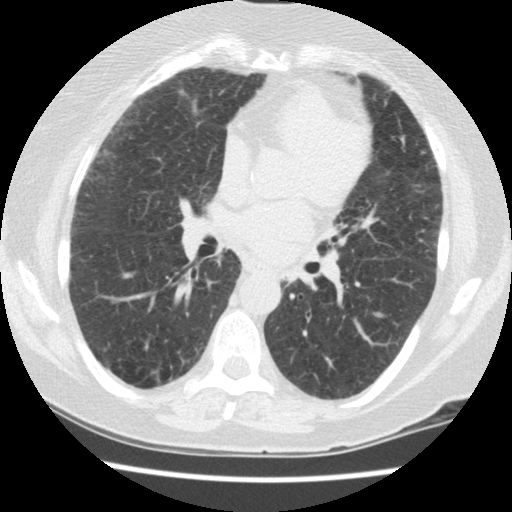
Chest CT (low-dose screening protocol), one axial image. Second screening round (one year after baseline). Lung window (W 1500 / L -600 HU). 2.5 mm slice thickness. 120 kVp. Slice 67 of 134 in the series. 512 × 512 image matrix, field of view 310 × 310 mm. Female, age 60 years at enrolment. Former smoker at enrolment.
Expert-annotated lung lesion, bounding box (x1, y1, x2, y2) in pixels: (271, 254, 317, 299). Screening reader's record for this exam (one nodule recorded; not confirmed to be the boxed lesion): non-calcified nodule or mass ≥4 mm, left lower lobe, 5 × 4 mm, smooth margins, soft tissue attenuation, pre-existing on the prior screen: yes; interval growth: no. Lung cancer was diagnosed 423 days after this screen (after the third annual screen): small cell carcinoma, NOS, left lower lobe, undifferentiated (G4), stage IV (AJCC 6th edition), 69 mm at pathology.